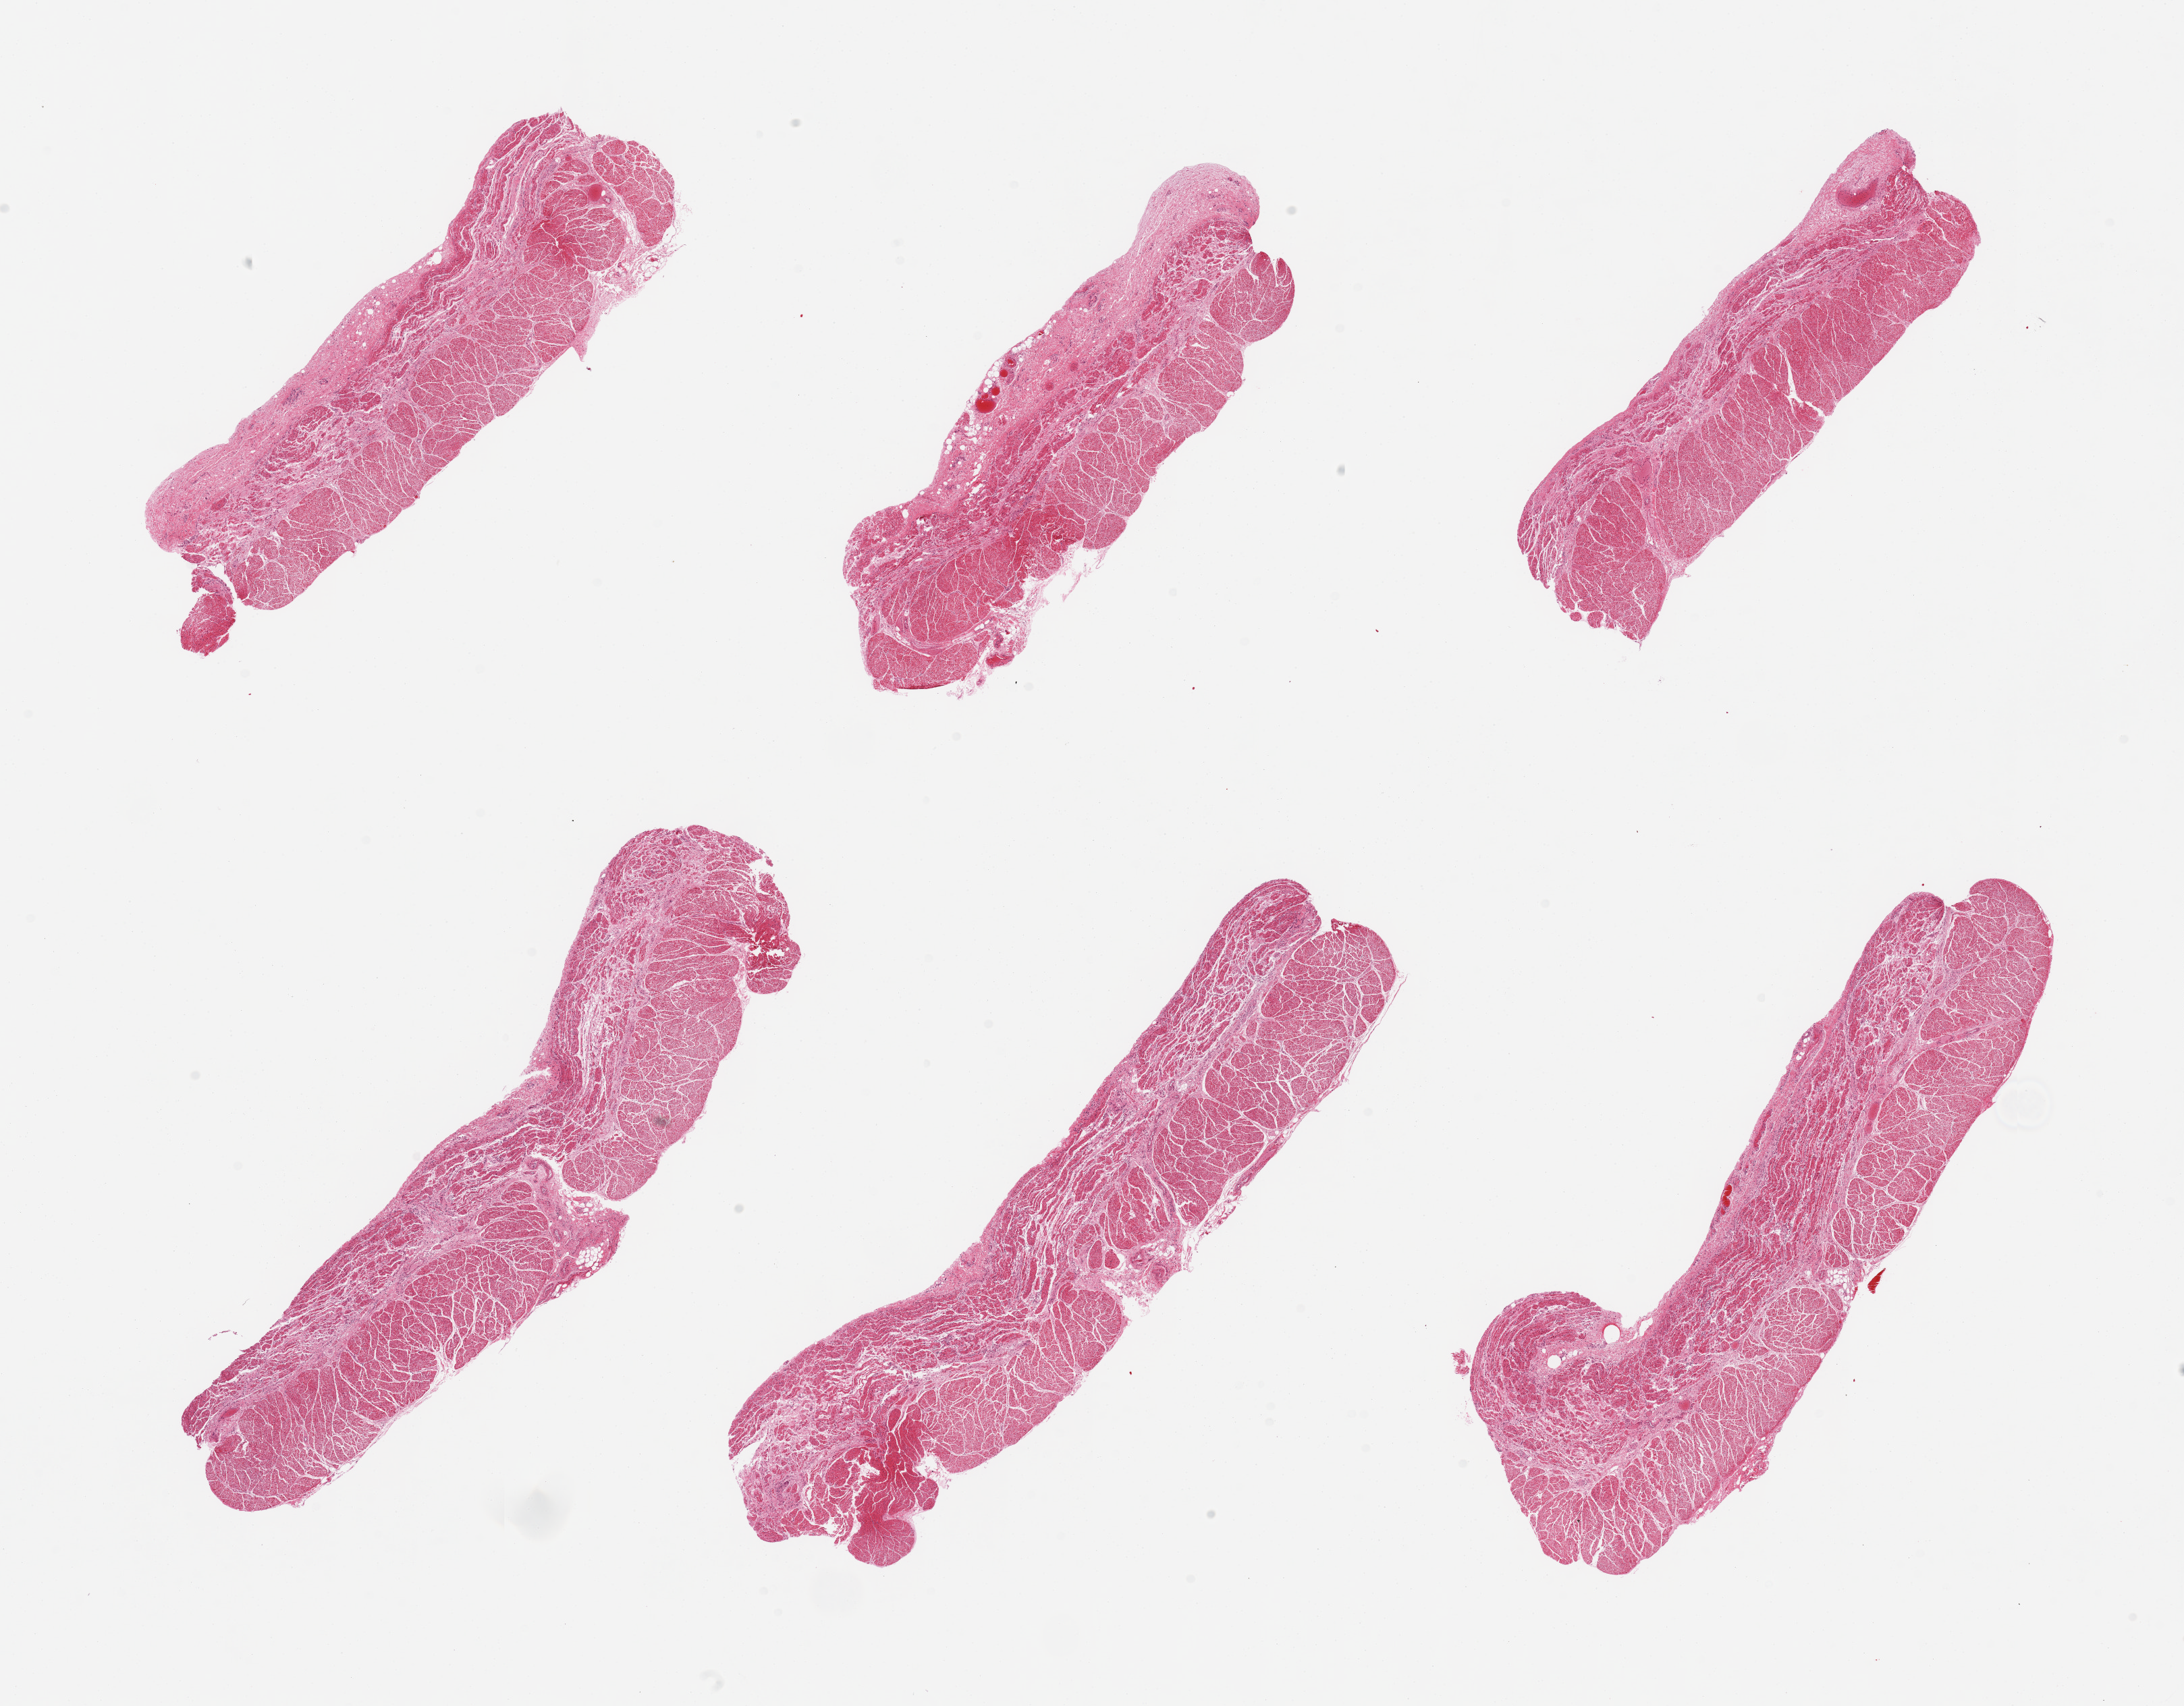
Haematoxylin and eosin whole-slide image — whole scanned area (about 25.6 x 20.0 mm) shown as a low-resolution overview, PAXgene-fixed paraffin-embedded (PFPE) section, section of esophageal muscle (target tissue), donor tissue sample. Male donor.
Review note (as recorded): 6 pieces, well trimmed.